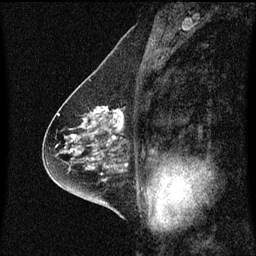
Breast MRI (dynamic contrast-enhanced), one sagittal slice. Slice 34 of 60 in the series (ordered by position). Dynamic contrast-enhanced series, image 2 of 3 at this slice position (ordered by acquisition). 1.5 T. TE 4.2 ms, TR 8.4 ms. 2 mm slice thickness. 256 × 256 image matrix, field of view 200 × 200 mm. Female patient, age 58 years.
Annotated regions visible in this slice (semi-automatic segmentation, software-assisted and operator-edited):
- analysis volume of interest (the breast-tissue region the enhancement analysis was run in; not a lesion): box from (x=86, y=106) to (x=129, y=143) px
- tumour enhancement mask (voxels above the 70 % enhancement threshold inside the analysis volume of interest): (x=90, y=106)–(x=124, y=141)